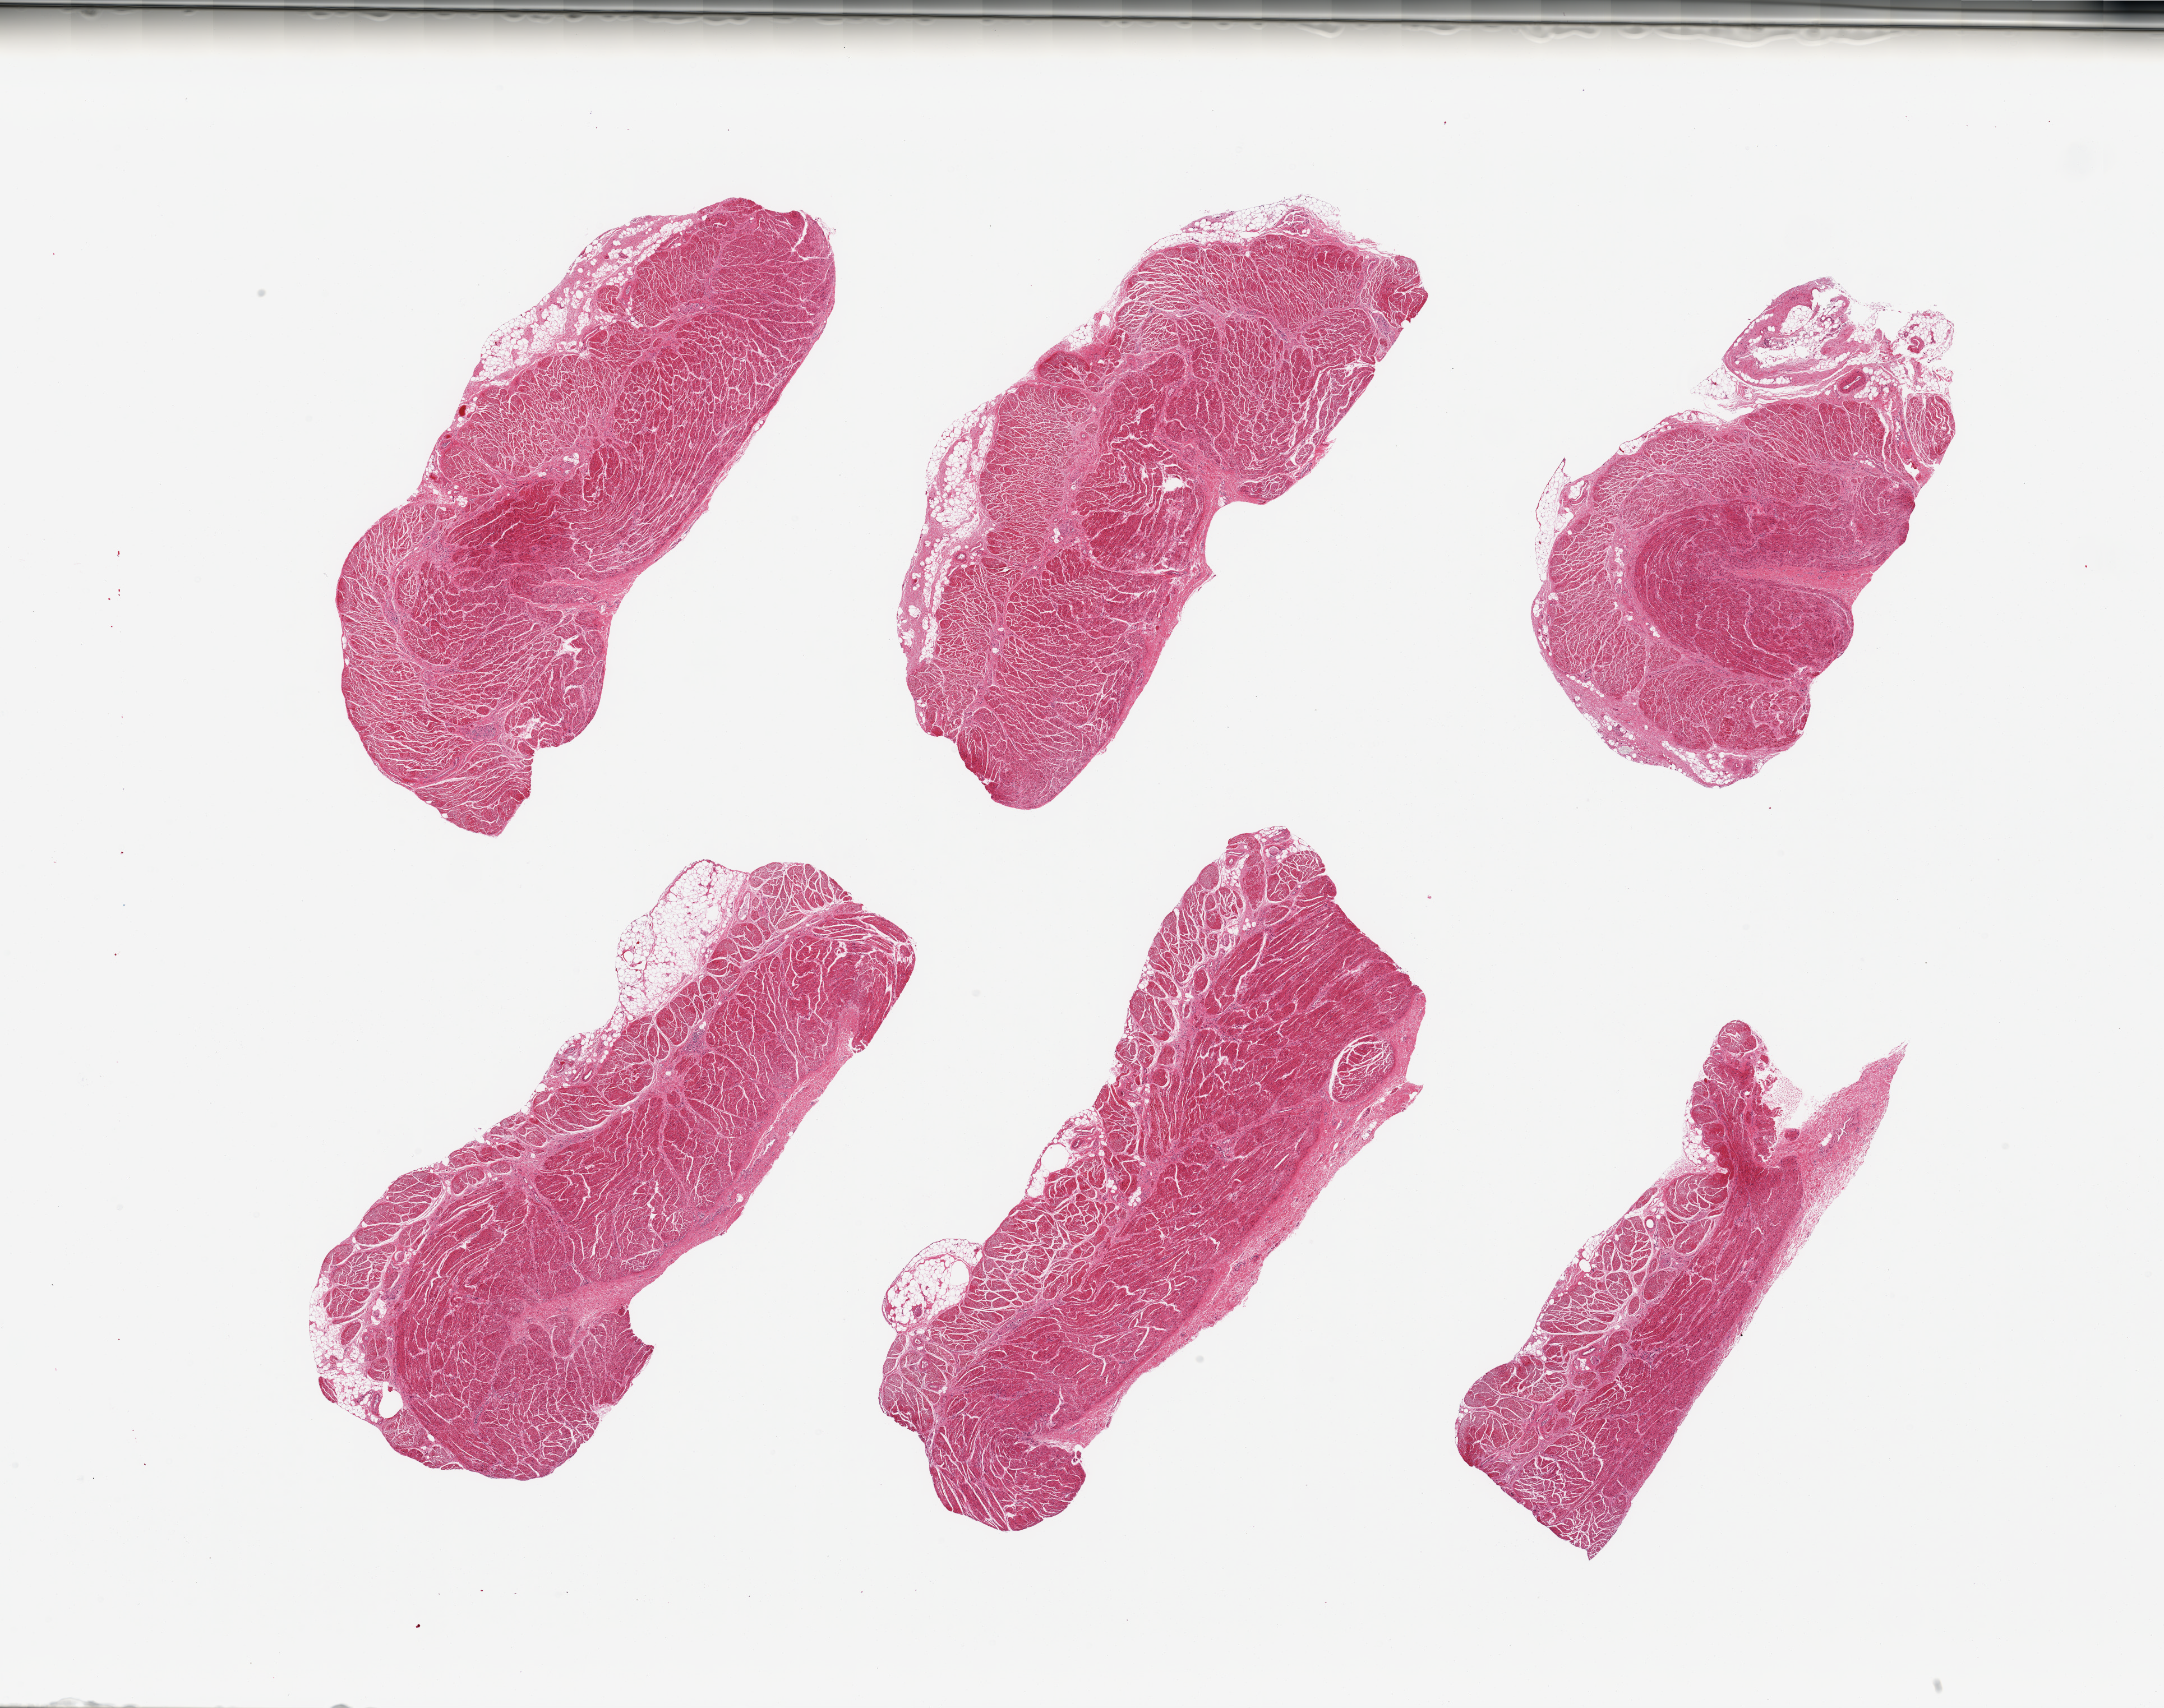
Whole-slide image, hematoxylin and eosin (H&E) stain, brightfield — shown as a low-resolution overview of the whole scanned area (about 30.5 x 24.1 mm, slide scanned at 20x), PAXgene-fixed paraffin-embedded (PFPE) section, sampled site (target tissue): gastroesophageal junction, donor tissue sample. Donor sex: male.
Pathologist's review note for this sample: 6 pieces; target muscularis with rim of serosa.